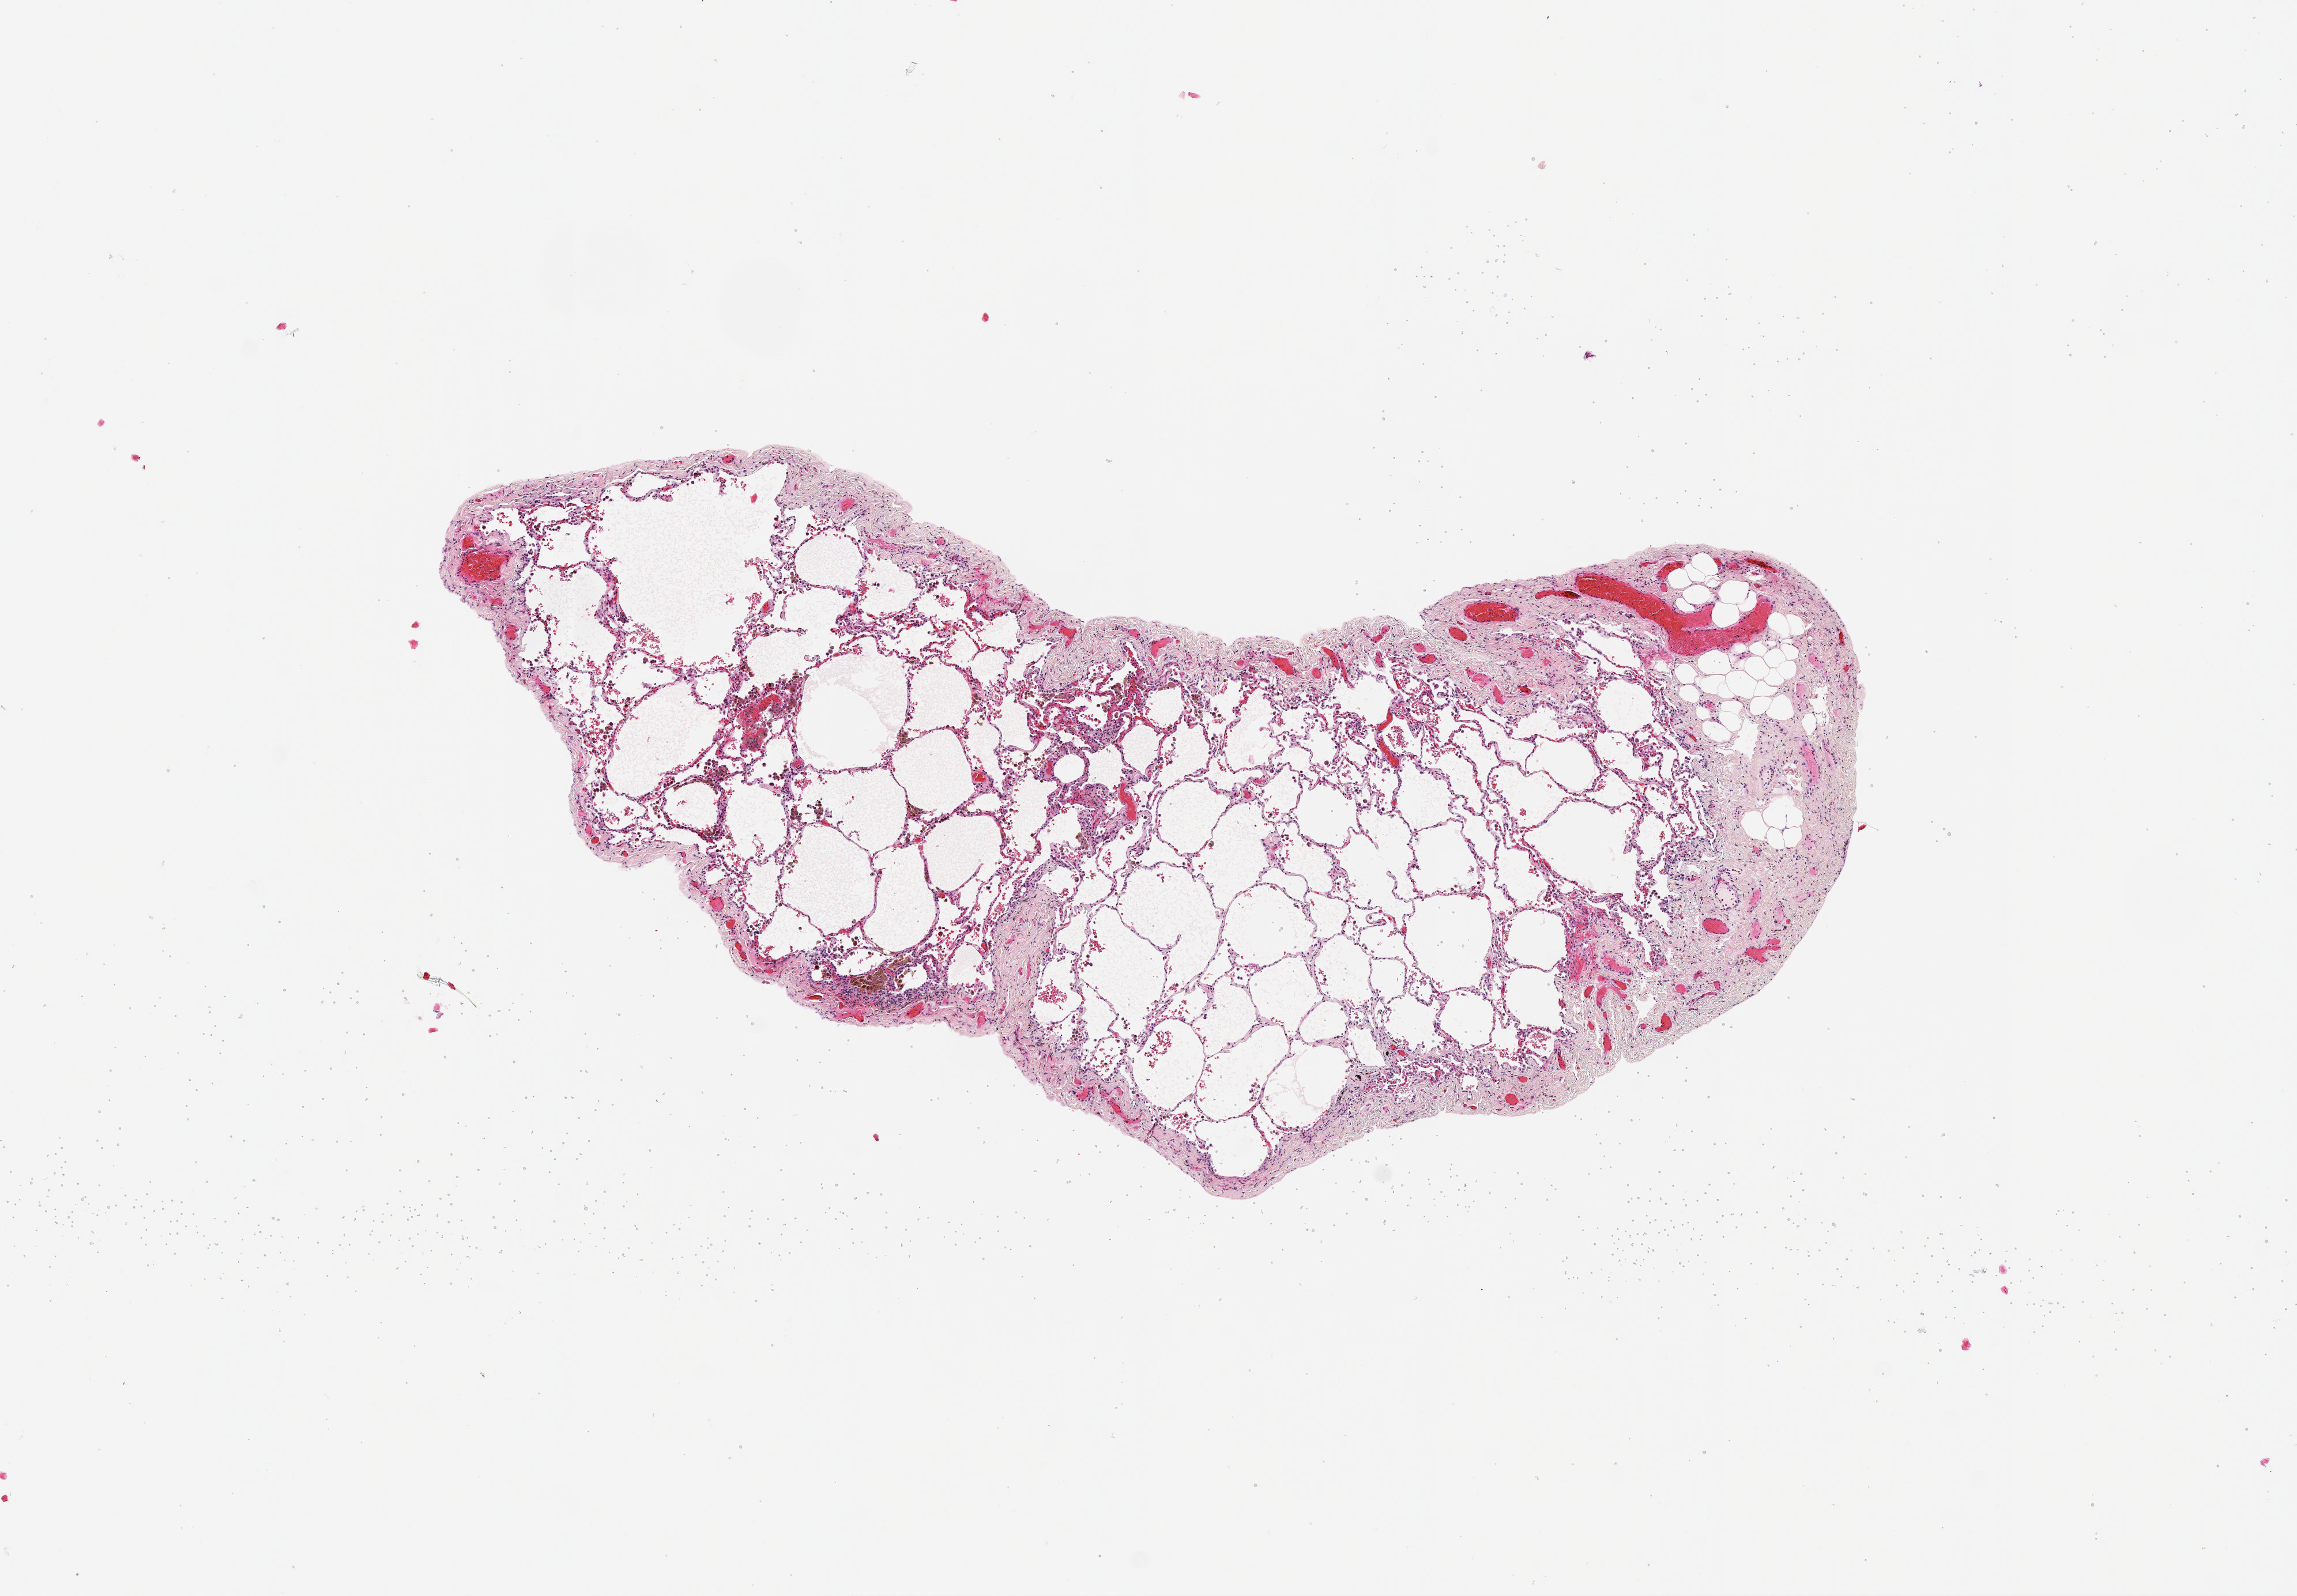
Whole-slide histology image, H&E — whole scanned area (about 8.0 x 5.6 mm) shown as a low-resolution overview; lung, normal (non-tumour) tissue. 62-year-old male patient.
This section: normal (non-tumour) tissue from the same patient. Patient diagnosis (cohort enrolment): squamous cell carcinoma (lung).